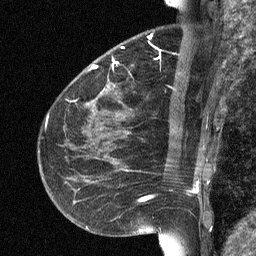
Breast MRI (dynamic contrast-enhanced), one sagittal slice. Position 24 of 64 along the scan axis. Dynamic contrast-enhanced study with each time point stored as its own series, time point 2 of 3 at this slice position (early post-contrast, ordered by acquisition time). 1.5 T. TE 4.8 ms, TR 27 ms. 2 mm slice thickness. 256 × 256 image matrix, field of view 180 × 180 mm. Female patient, age 51 years. Case-level facts recorded for this patient, not image findings: setting: breast cancer imaged before/during neoadjuvant chemotherapy; receptor status: HR-positive, HER2-negative.
Structures marked on this image (semi-automatically segmented with operator editing):
- analysis volume of interest (the breast-tissue region the enhancement analysis was run in; not a lesion): box from (x=72, y=34) to (x=182, y=118) px
- tumour enhancement mask (voxels above the 90 % enhancement threshold inside the analysis volume of interest): (x=92, y=65)–(x=97, y=69)